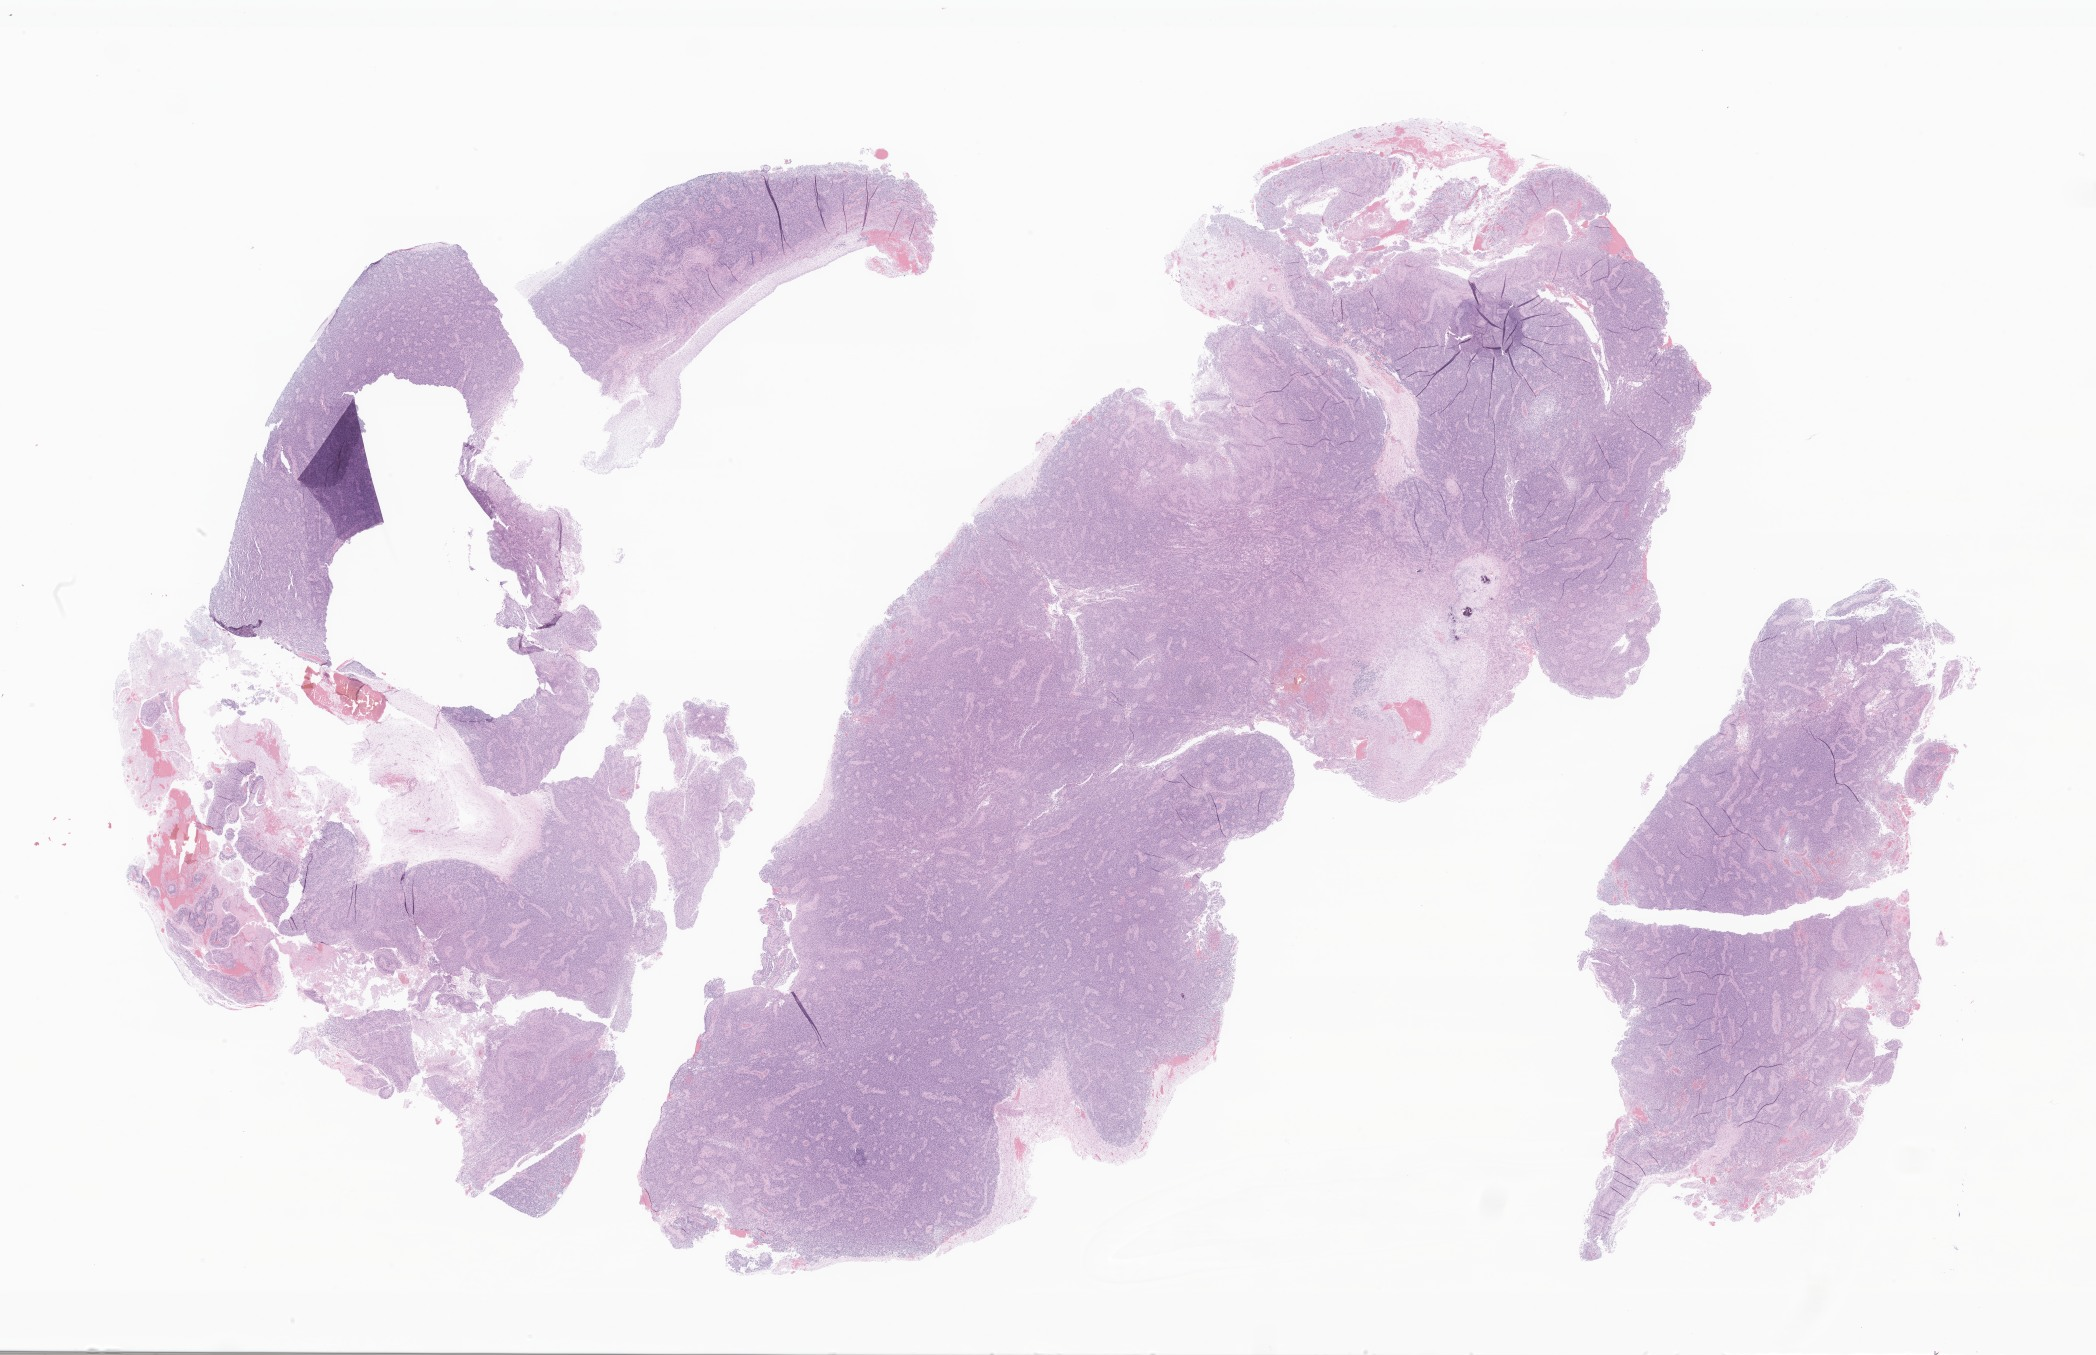
Whole-slide image, haematoxylin and eosin stain of tumor tissue from the brain — whole scanned area (about 35.4 x 22.9 mm) shown as a low-resolution overview, formalin-fixed, paraffin-embedded (FFPE) tissue. Patient: female, age 133 days.
Diagnosis: Ependymoma, NOS.